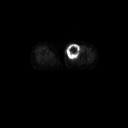
FDG PET of an extremity soft-tissue mass (from a PET/CT study), one axial slice; position 38 of 91 along the scan axis; 128 × 128 image matrix. Patient: female, 74 years. Case-level facts recorded for this patient, not image findings: histological type: pleomorphic leiomyosarcoma; grade: high; site of the primary tumour: left thigh.
Outlined on this slice (expert contour drawn on MRI and transferred to this co-registered scan by the dataset authors):
- gross tumour volume including surrounding oedema: box from (x=66, y=43) to (x=81, y=61) px
- gross tumour volume (mass): (x=66, y=43)–(x=80, y=60)